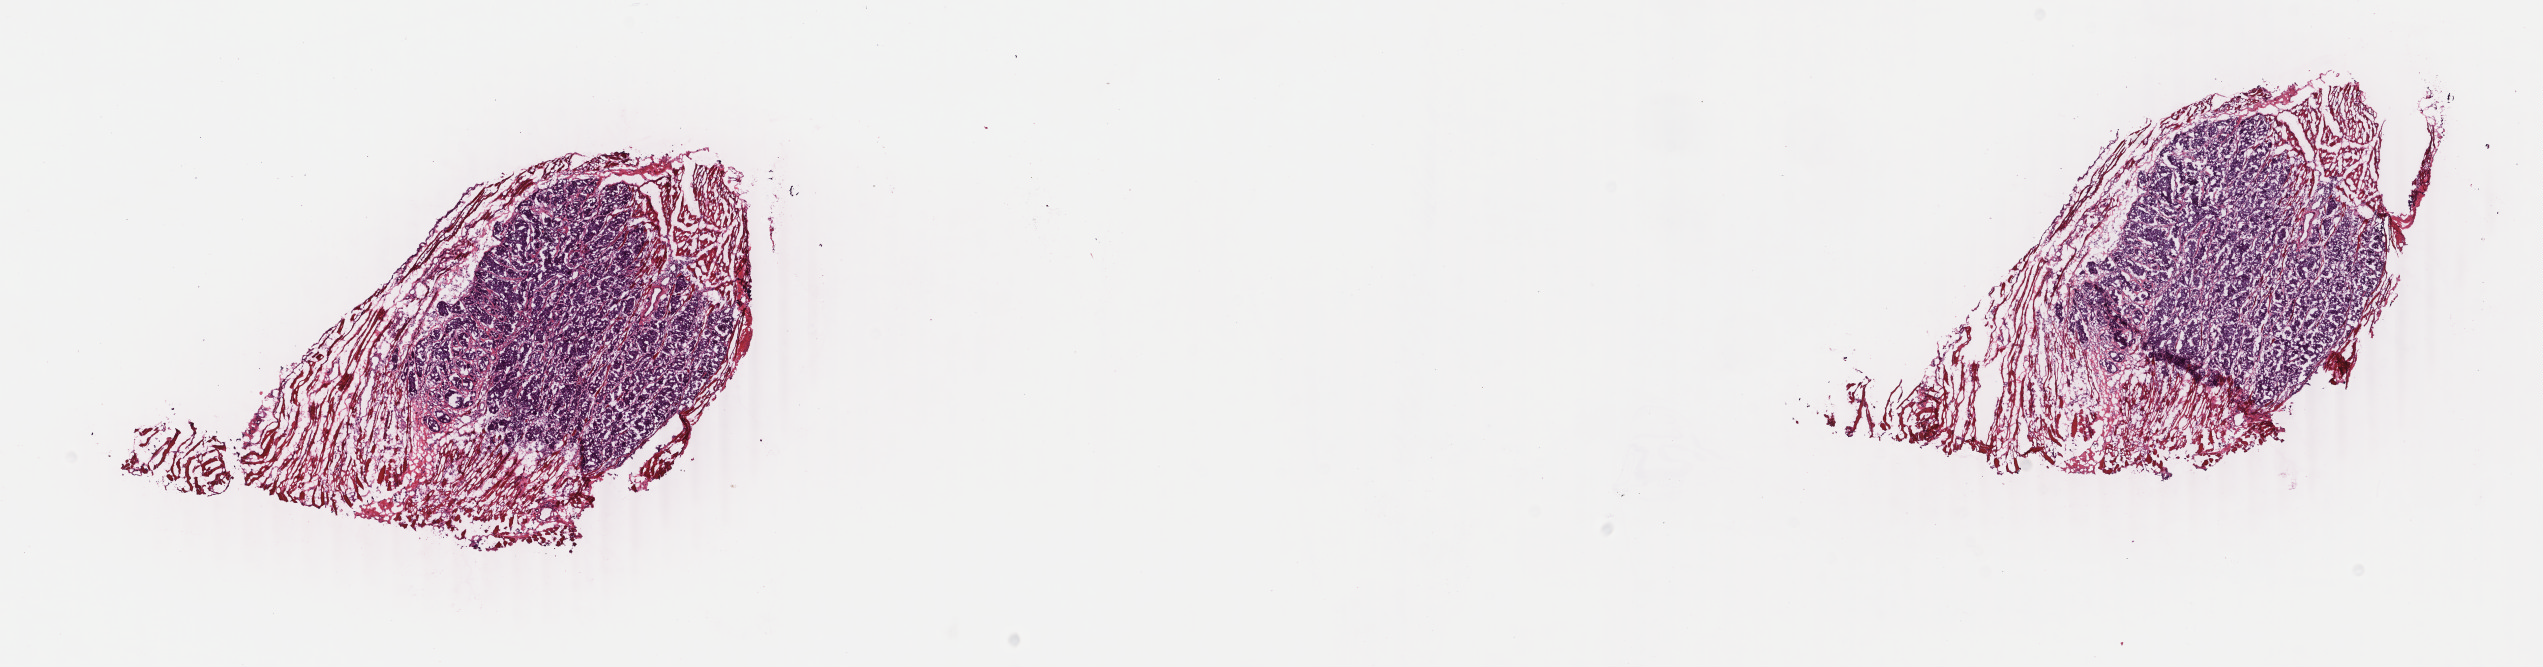
H&E-stained whole-slide image, shown as a low-resolution overview of the whole scanned area (about 20.2 x 5.3 mm); frozen section from the bottom of the tissue portion; primary tumour sample from the breast. Female, age 57 years at initial diagnosis. Composition of this section per pathologist review: tumour cells 75%, tumour nuclei 85%, normal cells 0%, stromal cells 25%, necrosis 0%. Infiltration values recorded for this section: lymphocyte infiltration 1%, monocyte infiltration 0%, neutrophil infiltration 0%.
Diagnosis: Infiltrating duct carcinoma, NOS.